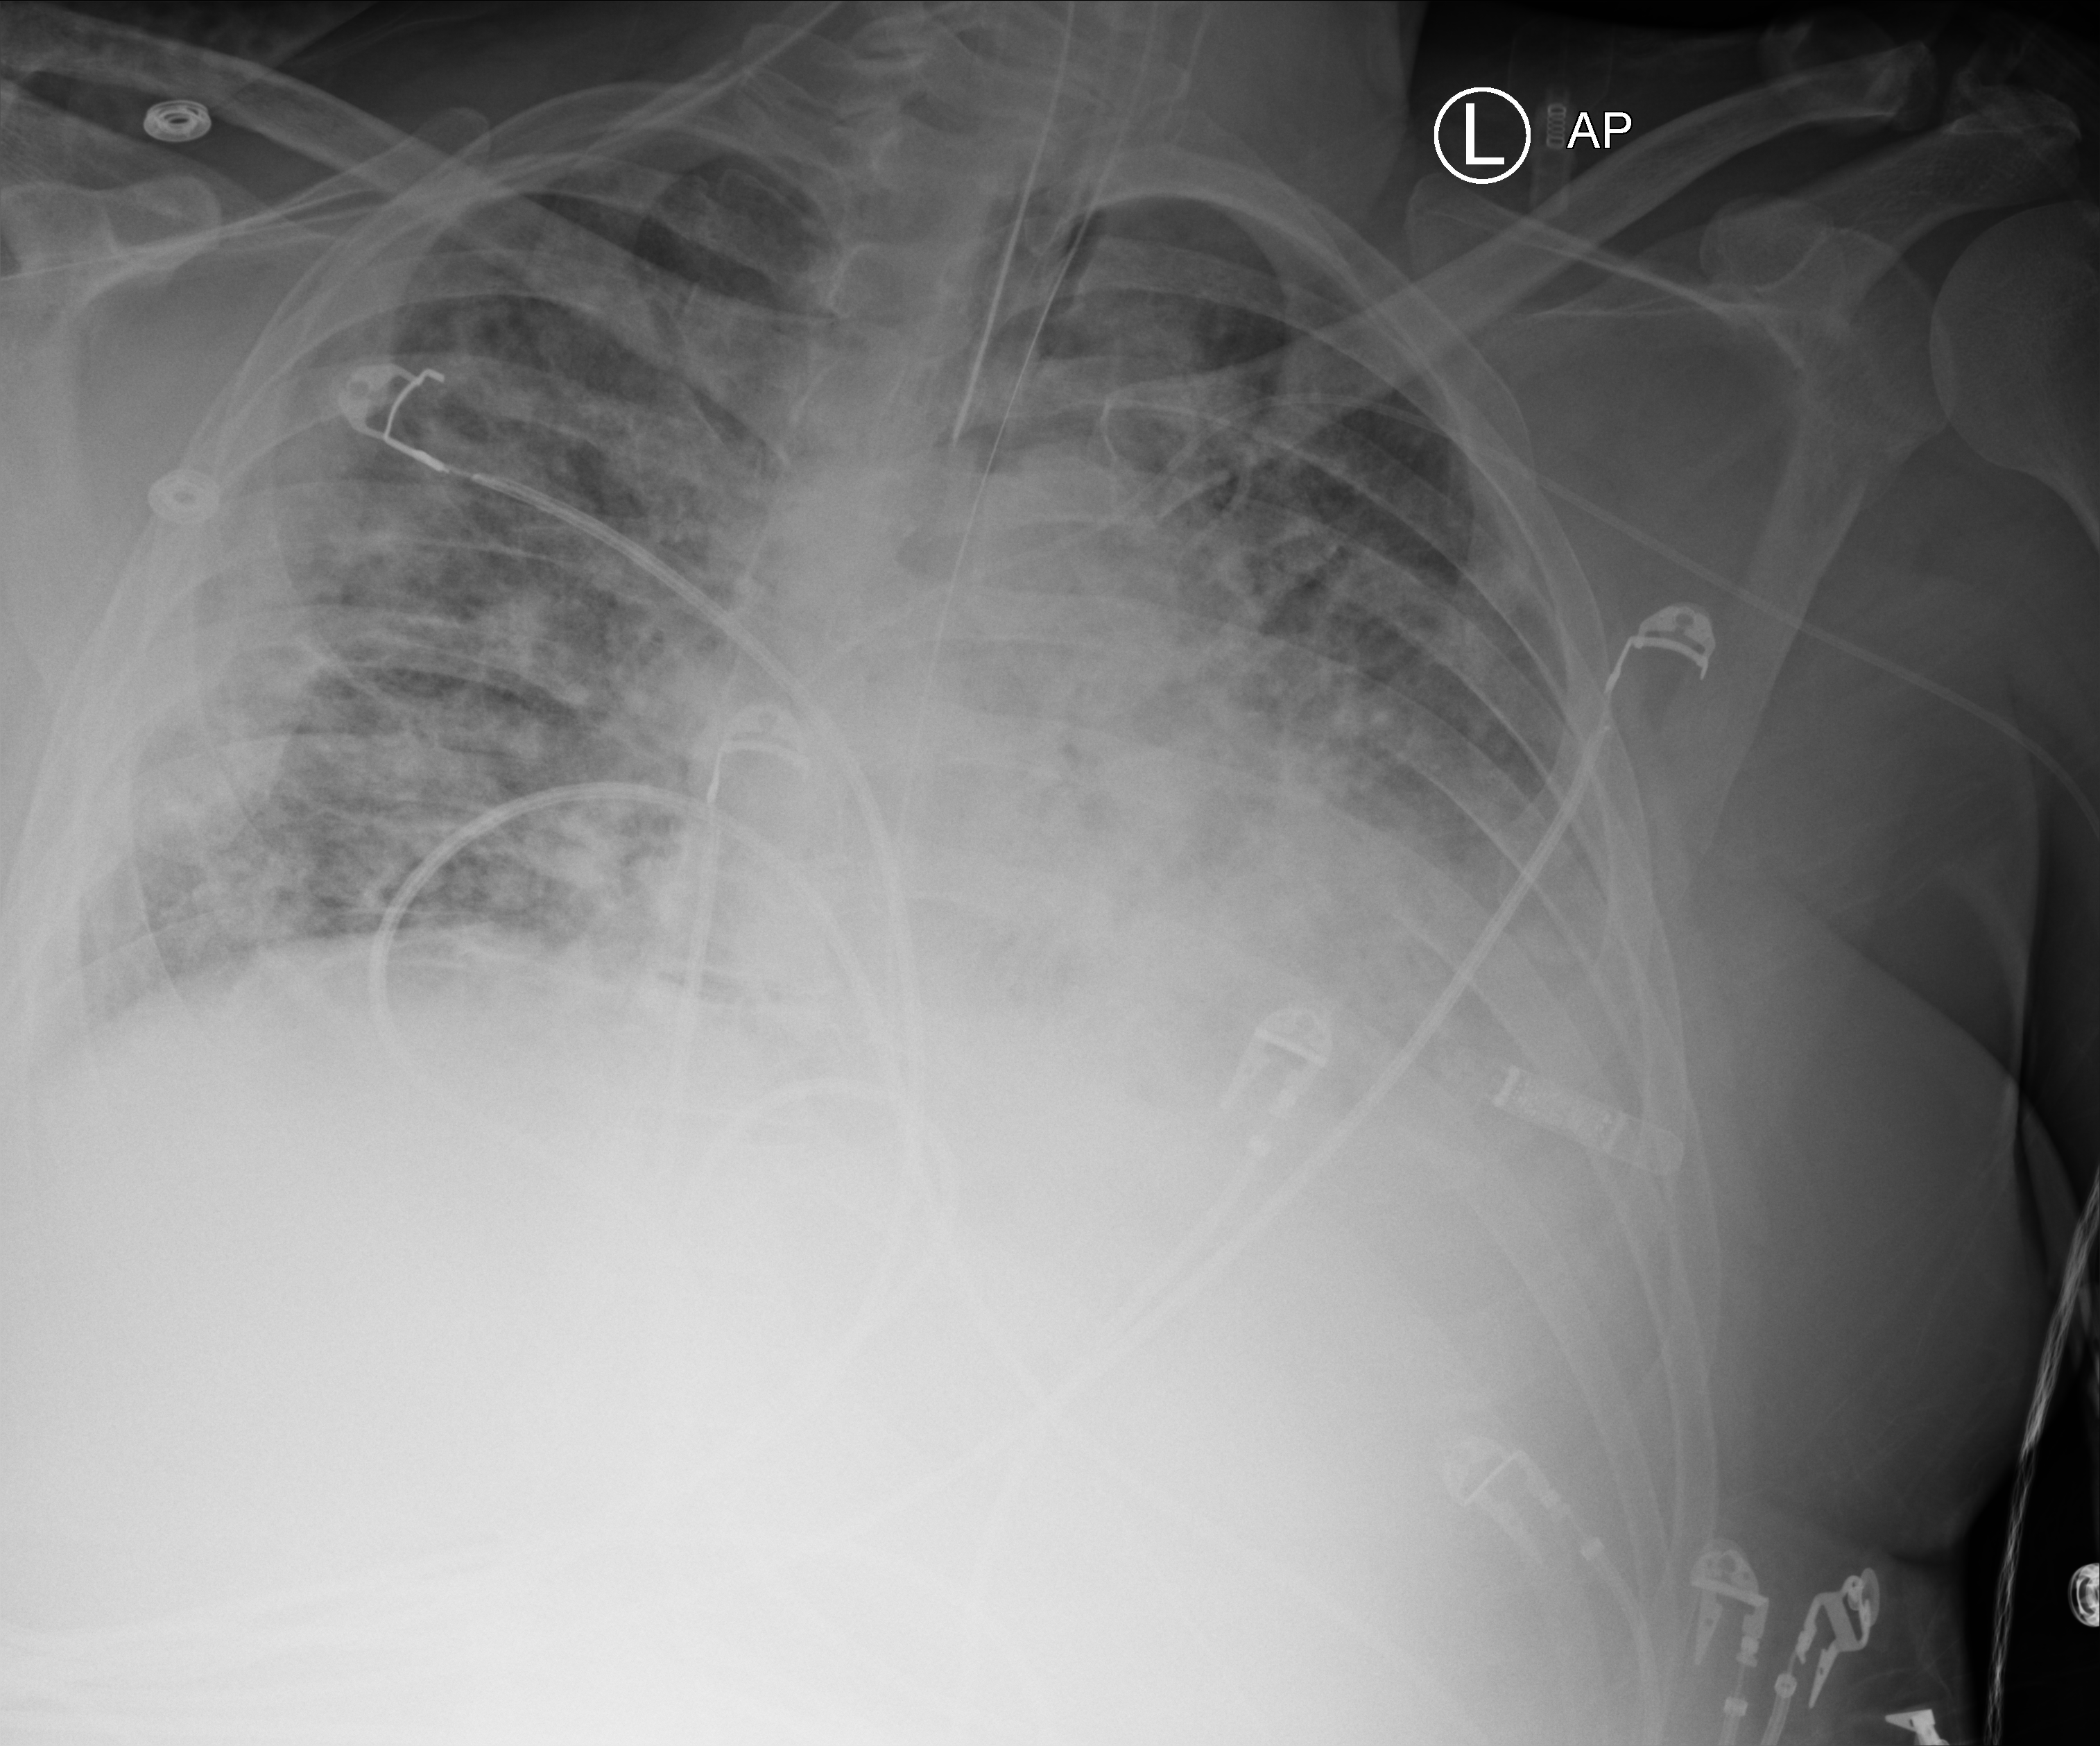
Chest X-ray (portable); anteroposterior (AP) projection. Patient hospitalised with COVID-19; male, aged 18–59 years.
From the hospital-stay record, not from the radiograph (when in the stay this image was taken is not recorded):
- chronic kidney disease (admission record): no
- admitted to intensive care during this hospital stay: yes